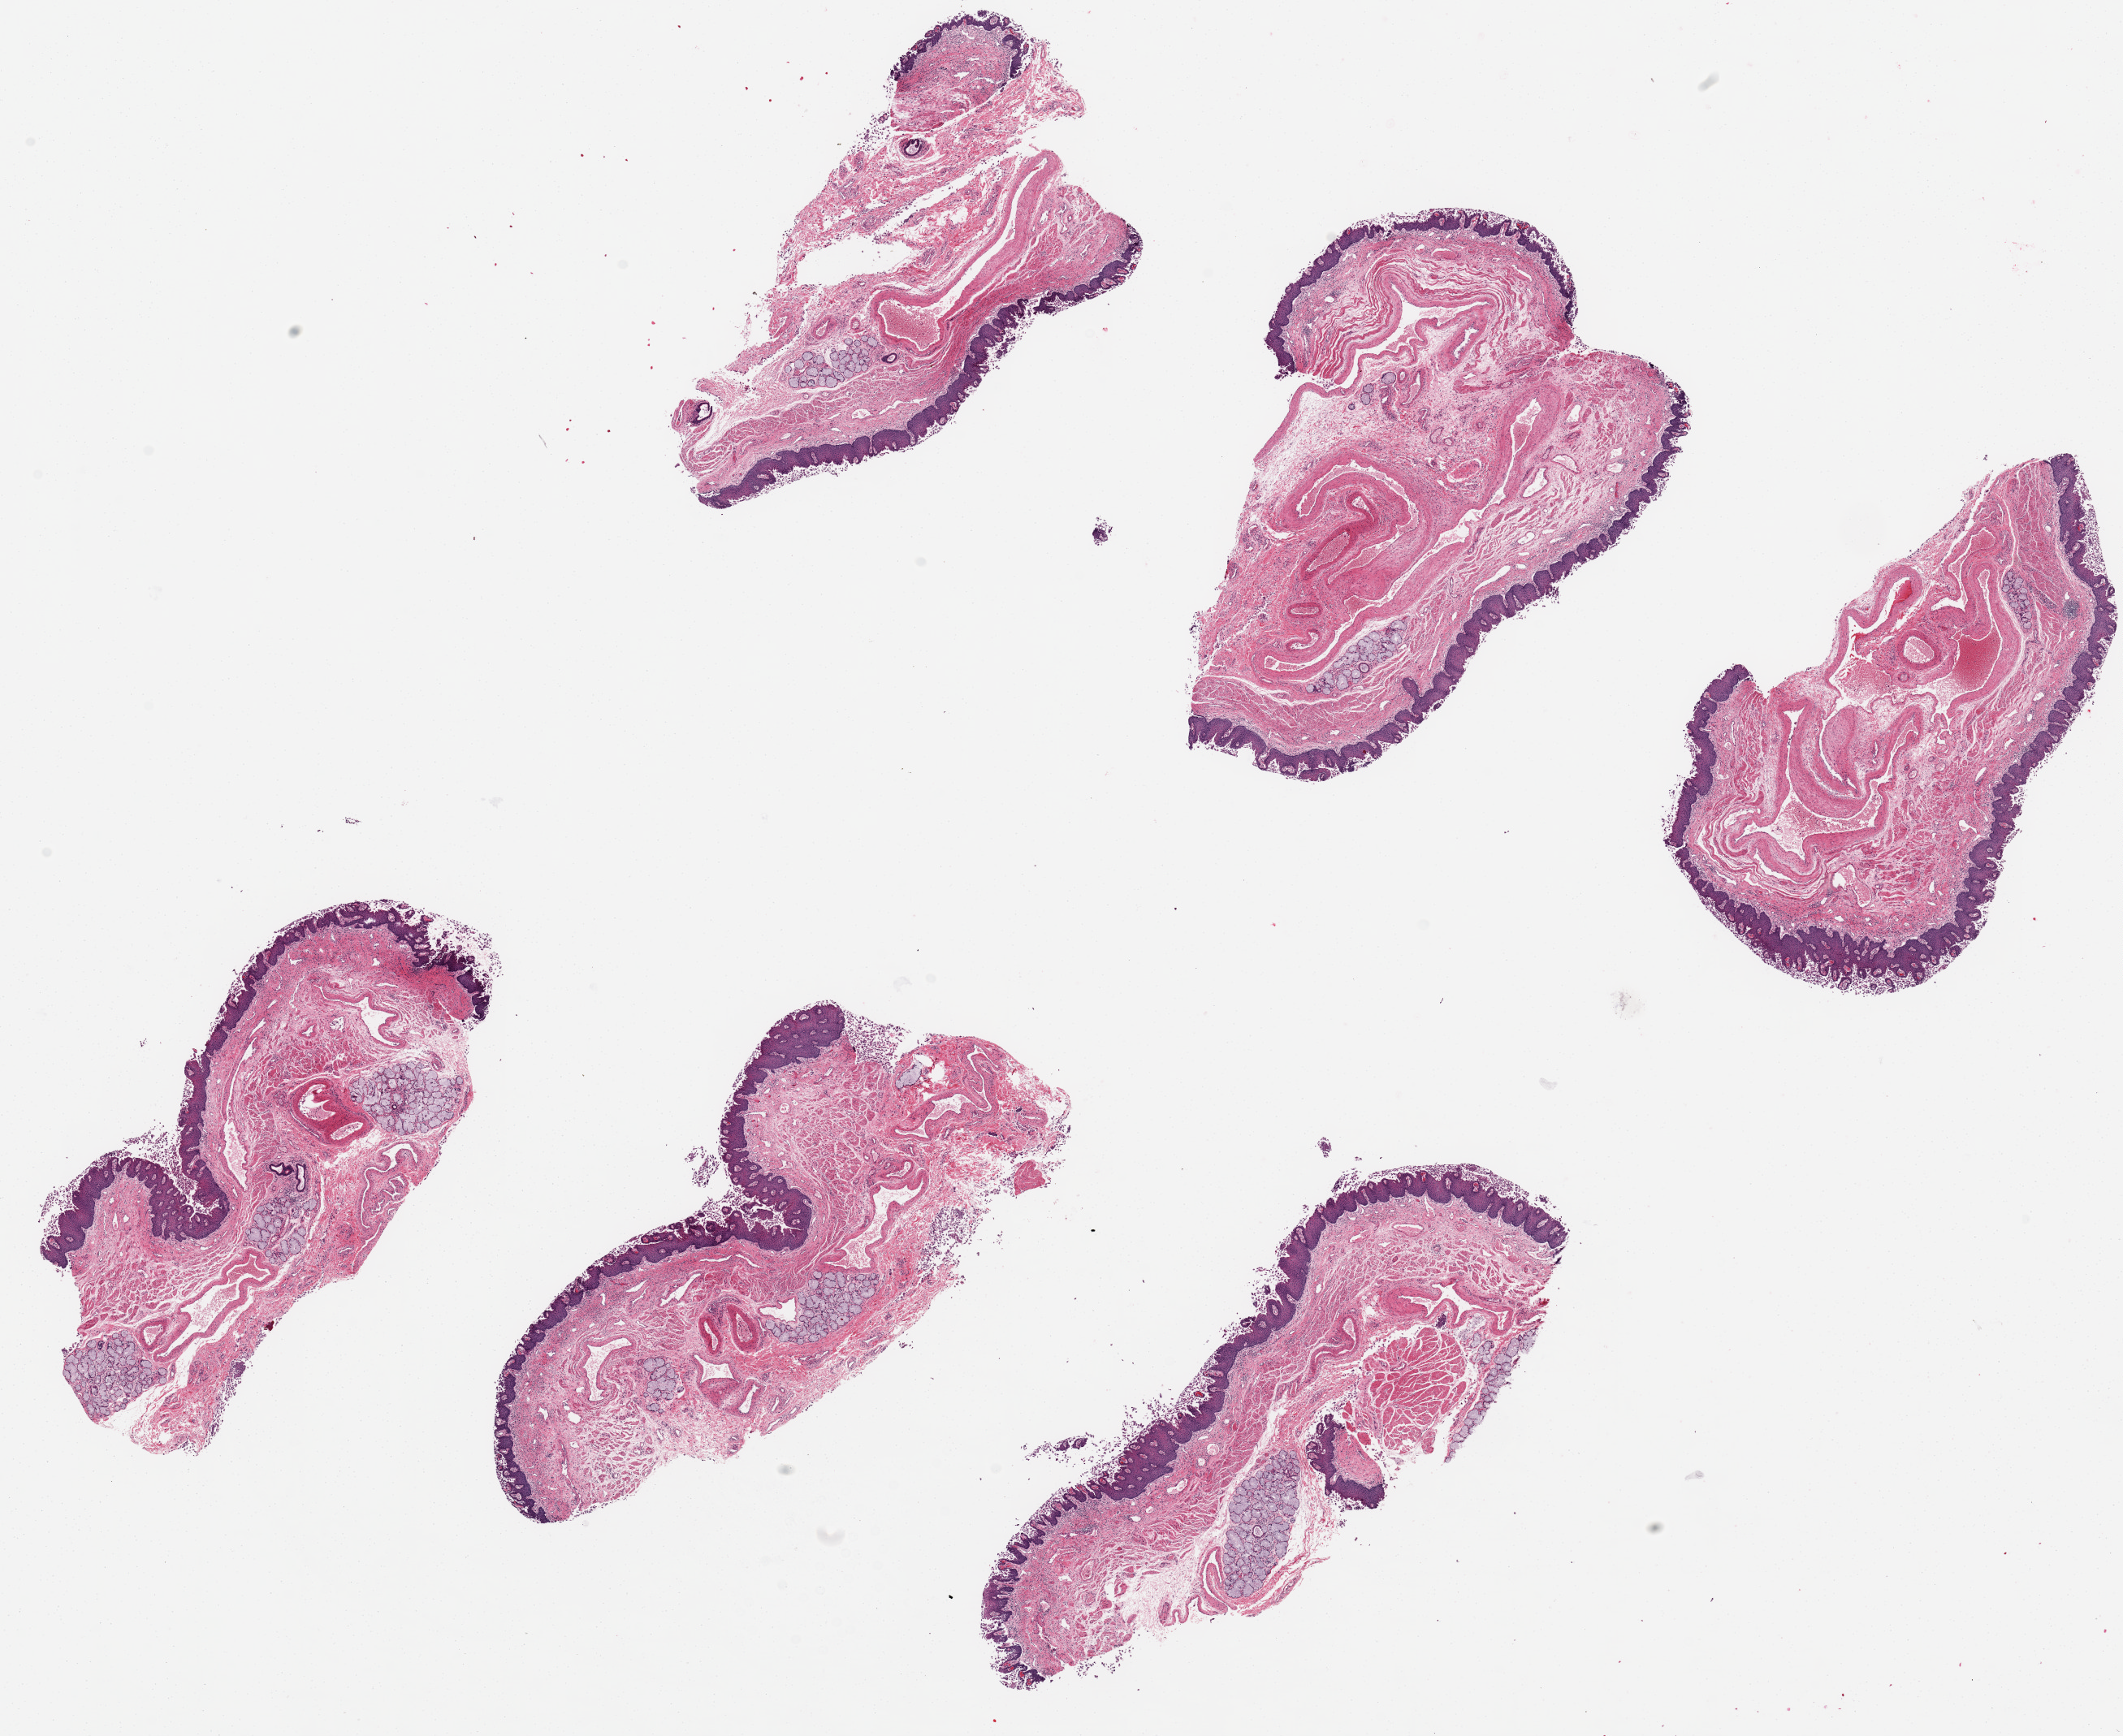
Whole-slide image, hematoxylin and eosin (H&E) stain — whole scanned area (about 20.7 x 16.9 mm, slide scanned at 20x) shown as a low-resolution overview, PAXgene-fixed, paraffin-embedded tissue, sampled site (target tissue): esophageal mucous membrane, donor tissue sample. Donor: female.
- review note (as recorded): 6 ~6x2mm pieces. Squamous mucosa is unusually poorly preserved with superficial sloughing; it is ~ 5-10% of thickness